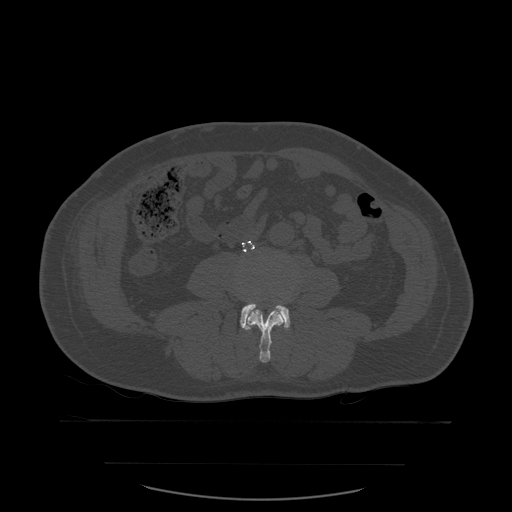
CT including the spine, one axial slice. Slice 180 of 590 in the series (ordered by position). Bone window (W 1800 / L 400 HU). 1.25 mm slice thickness. 512 × 512 image matrix, field of view 479 × 479 mm. Patient age 71 years. From the clinical record (not read from this slice): primary cancer: lung.
Structures marked on this image (semi-automatically segmented with operator editing):
- L3 vertebra: bounding box [x1, y1, x2, y2] px = [247, 310, 285, 363]
- L4 vertebra: [240, 303, 291, 330]